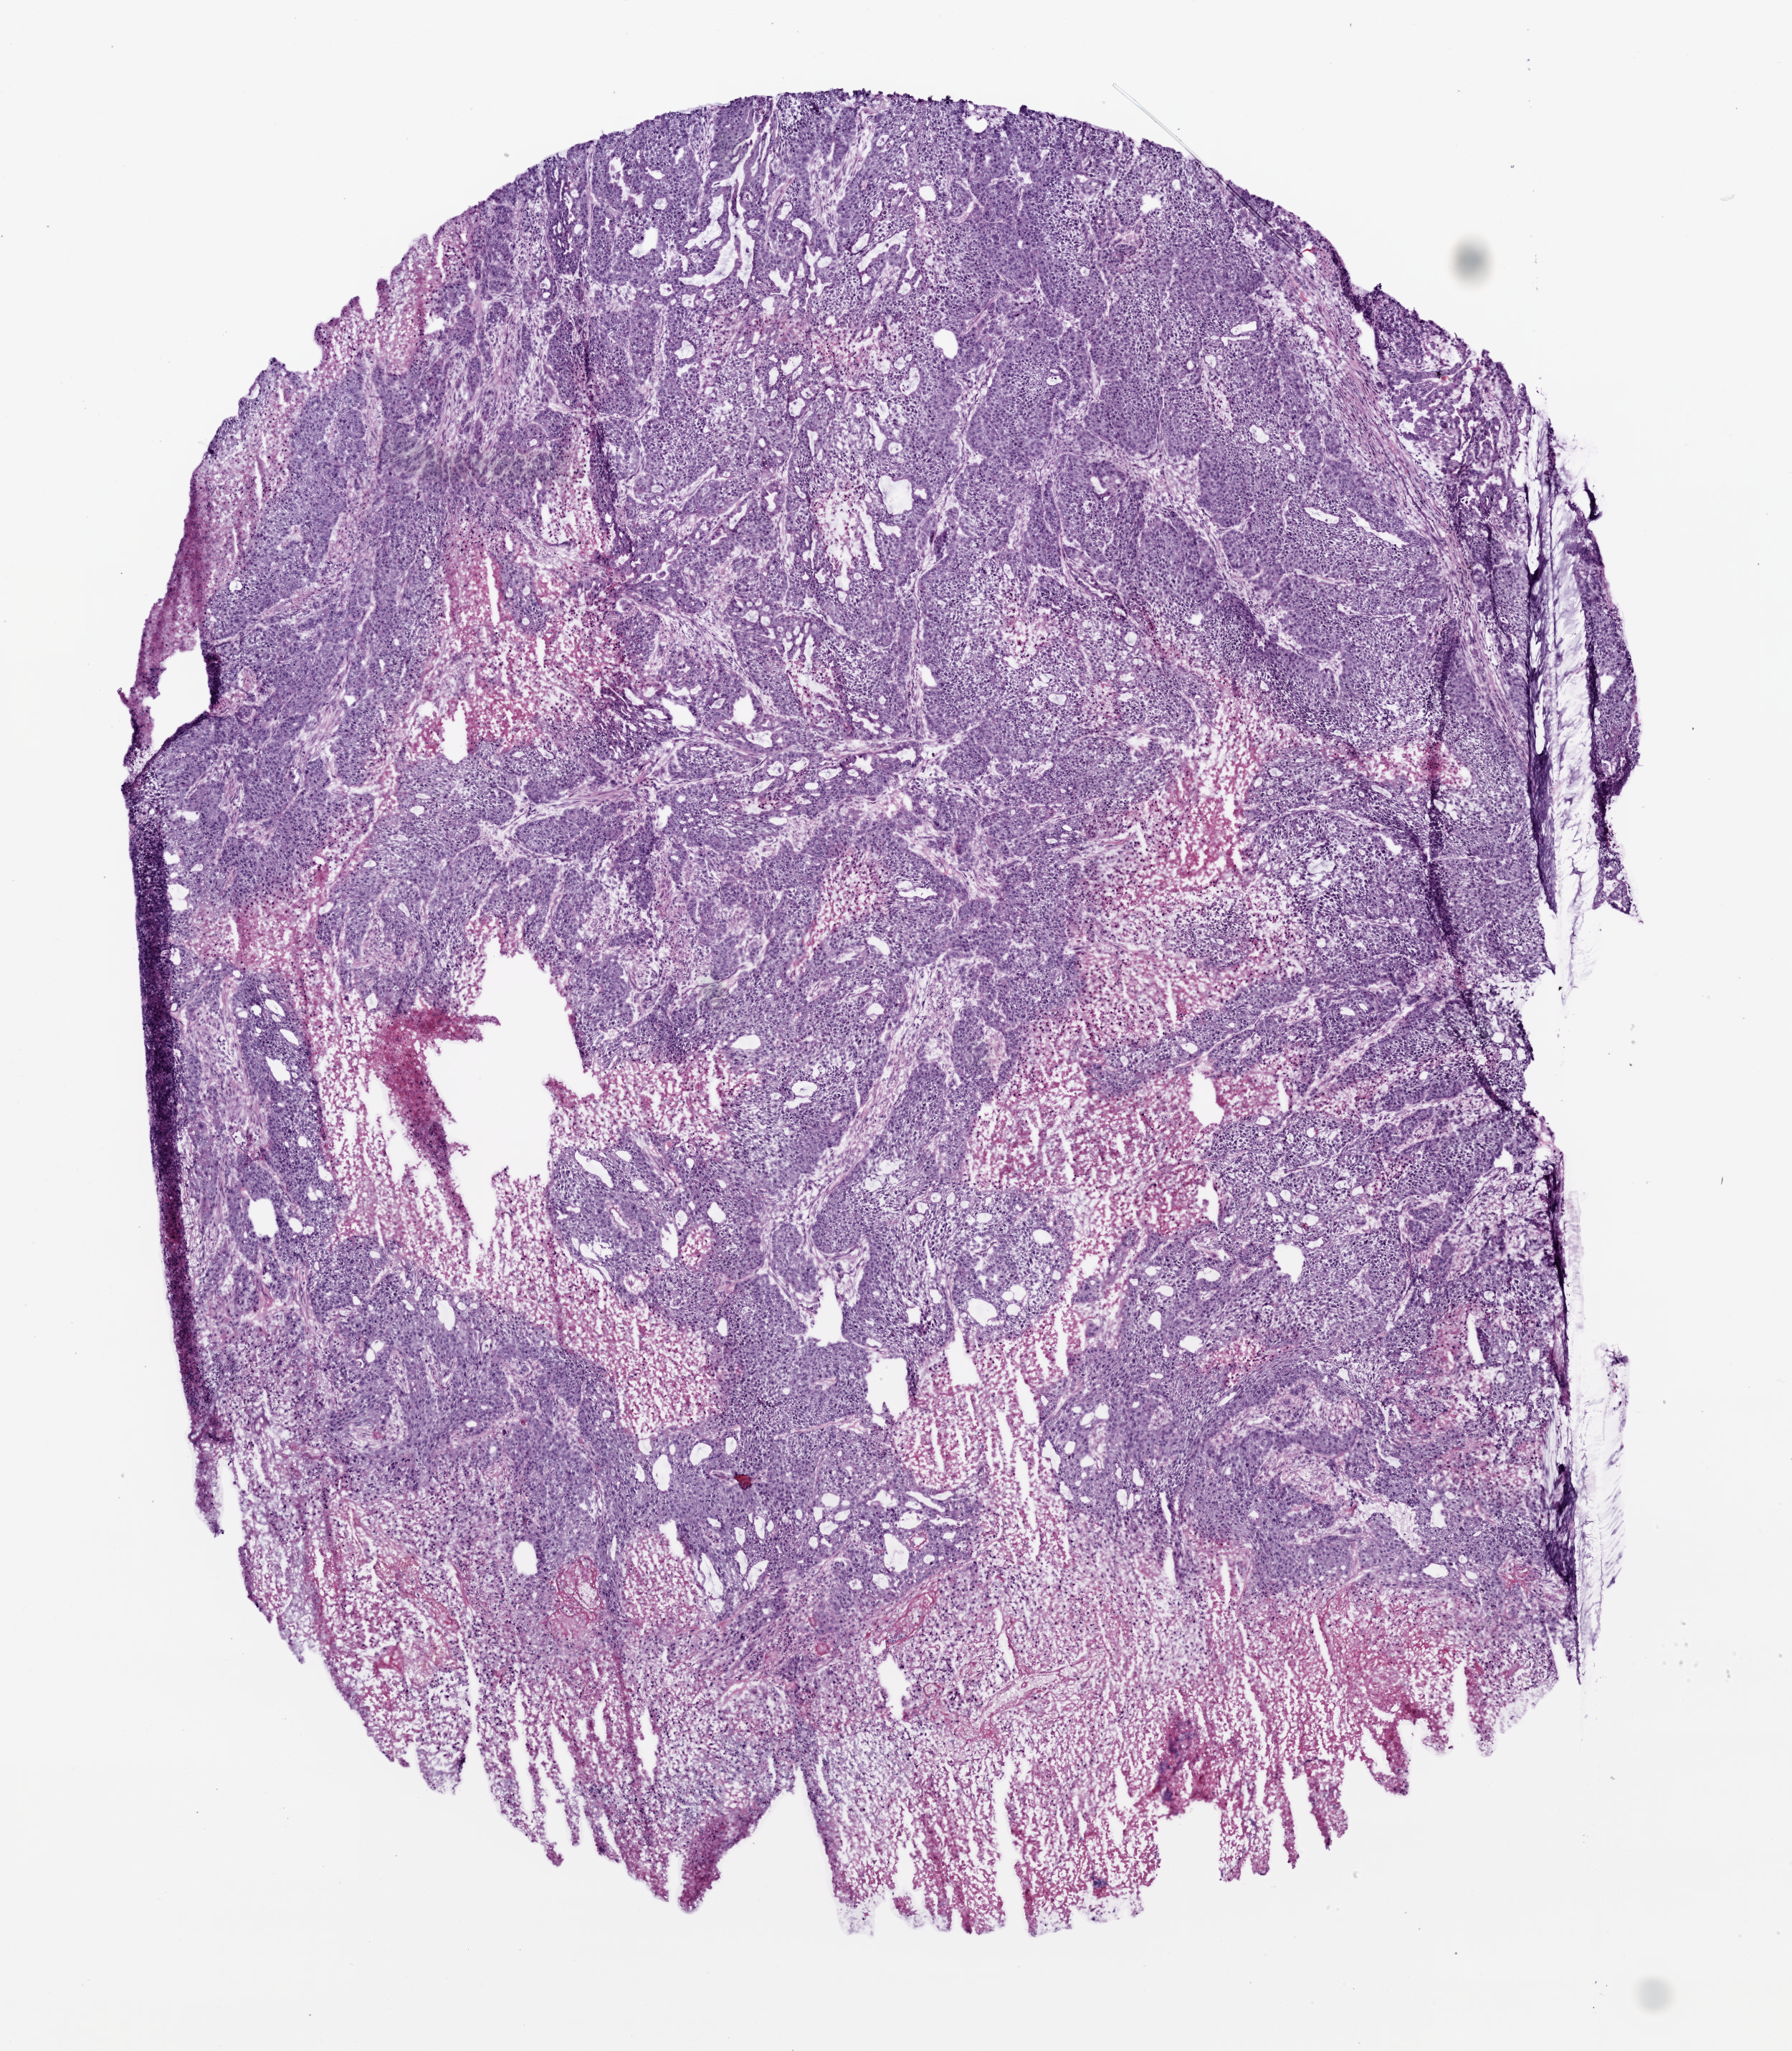
Whole-slide histology image, H&E-stained — shown as a low-resolution overview of the whole scanned area (about 5.0 x 5.7 mm, slide scanned at 20x); frozen section from the top of the tissue portion; sample: primary tumour, stomach. Male patient; age at initial diagnosis 85 years. Histologic grade: G3 (poorly differentiated). Pathologist review of this section (percent, as recorded): tumour cells 77%, tumour nuclei 75%, normal cells 0%, stromal cells 5%, necrosis 18%.
Histologic diagnosis: Adenocarcinoma, intestinal type (gastric antrum). Lymph nodes positive (case pathology): 0 of 27 examined. AJCC pathologic stage: IB (5th edition).